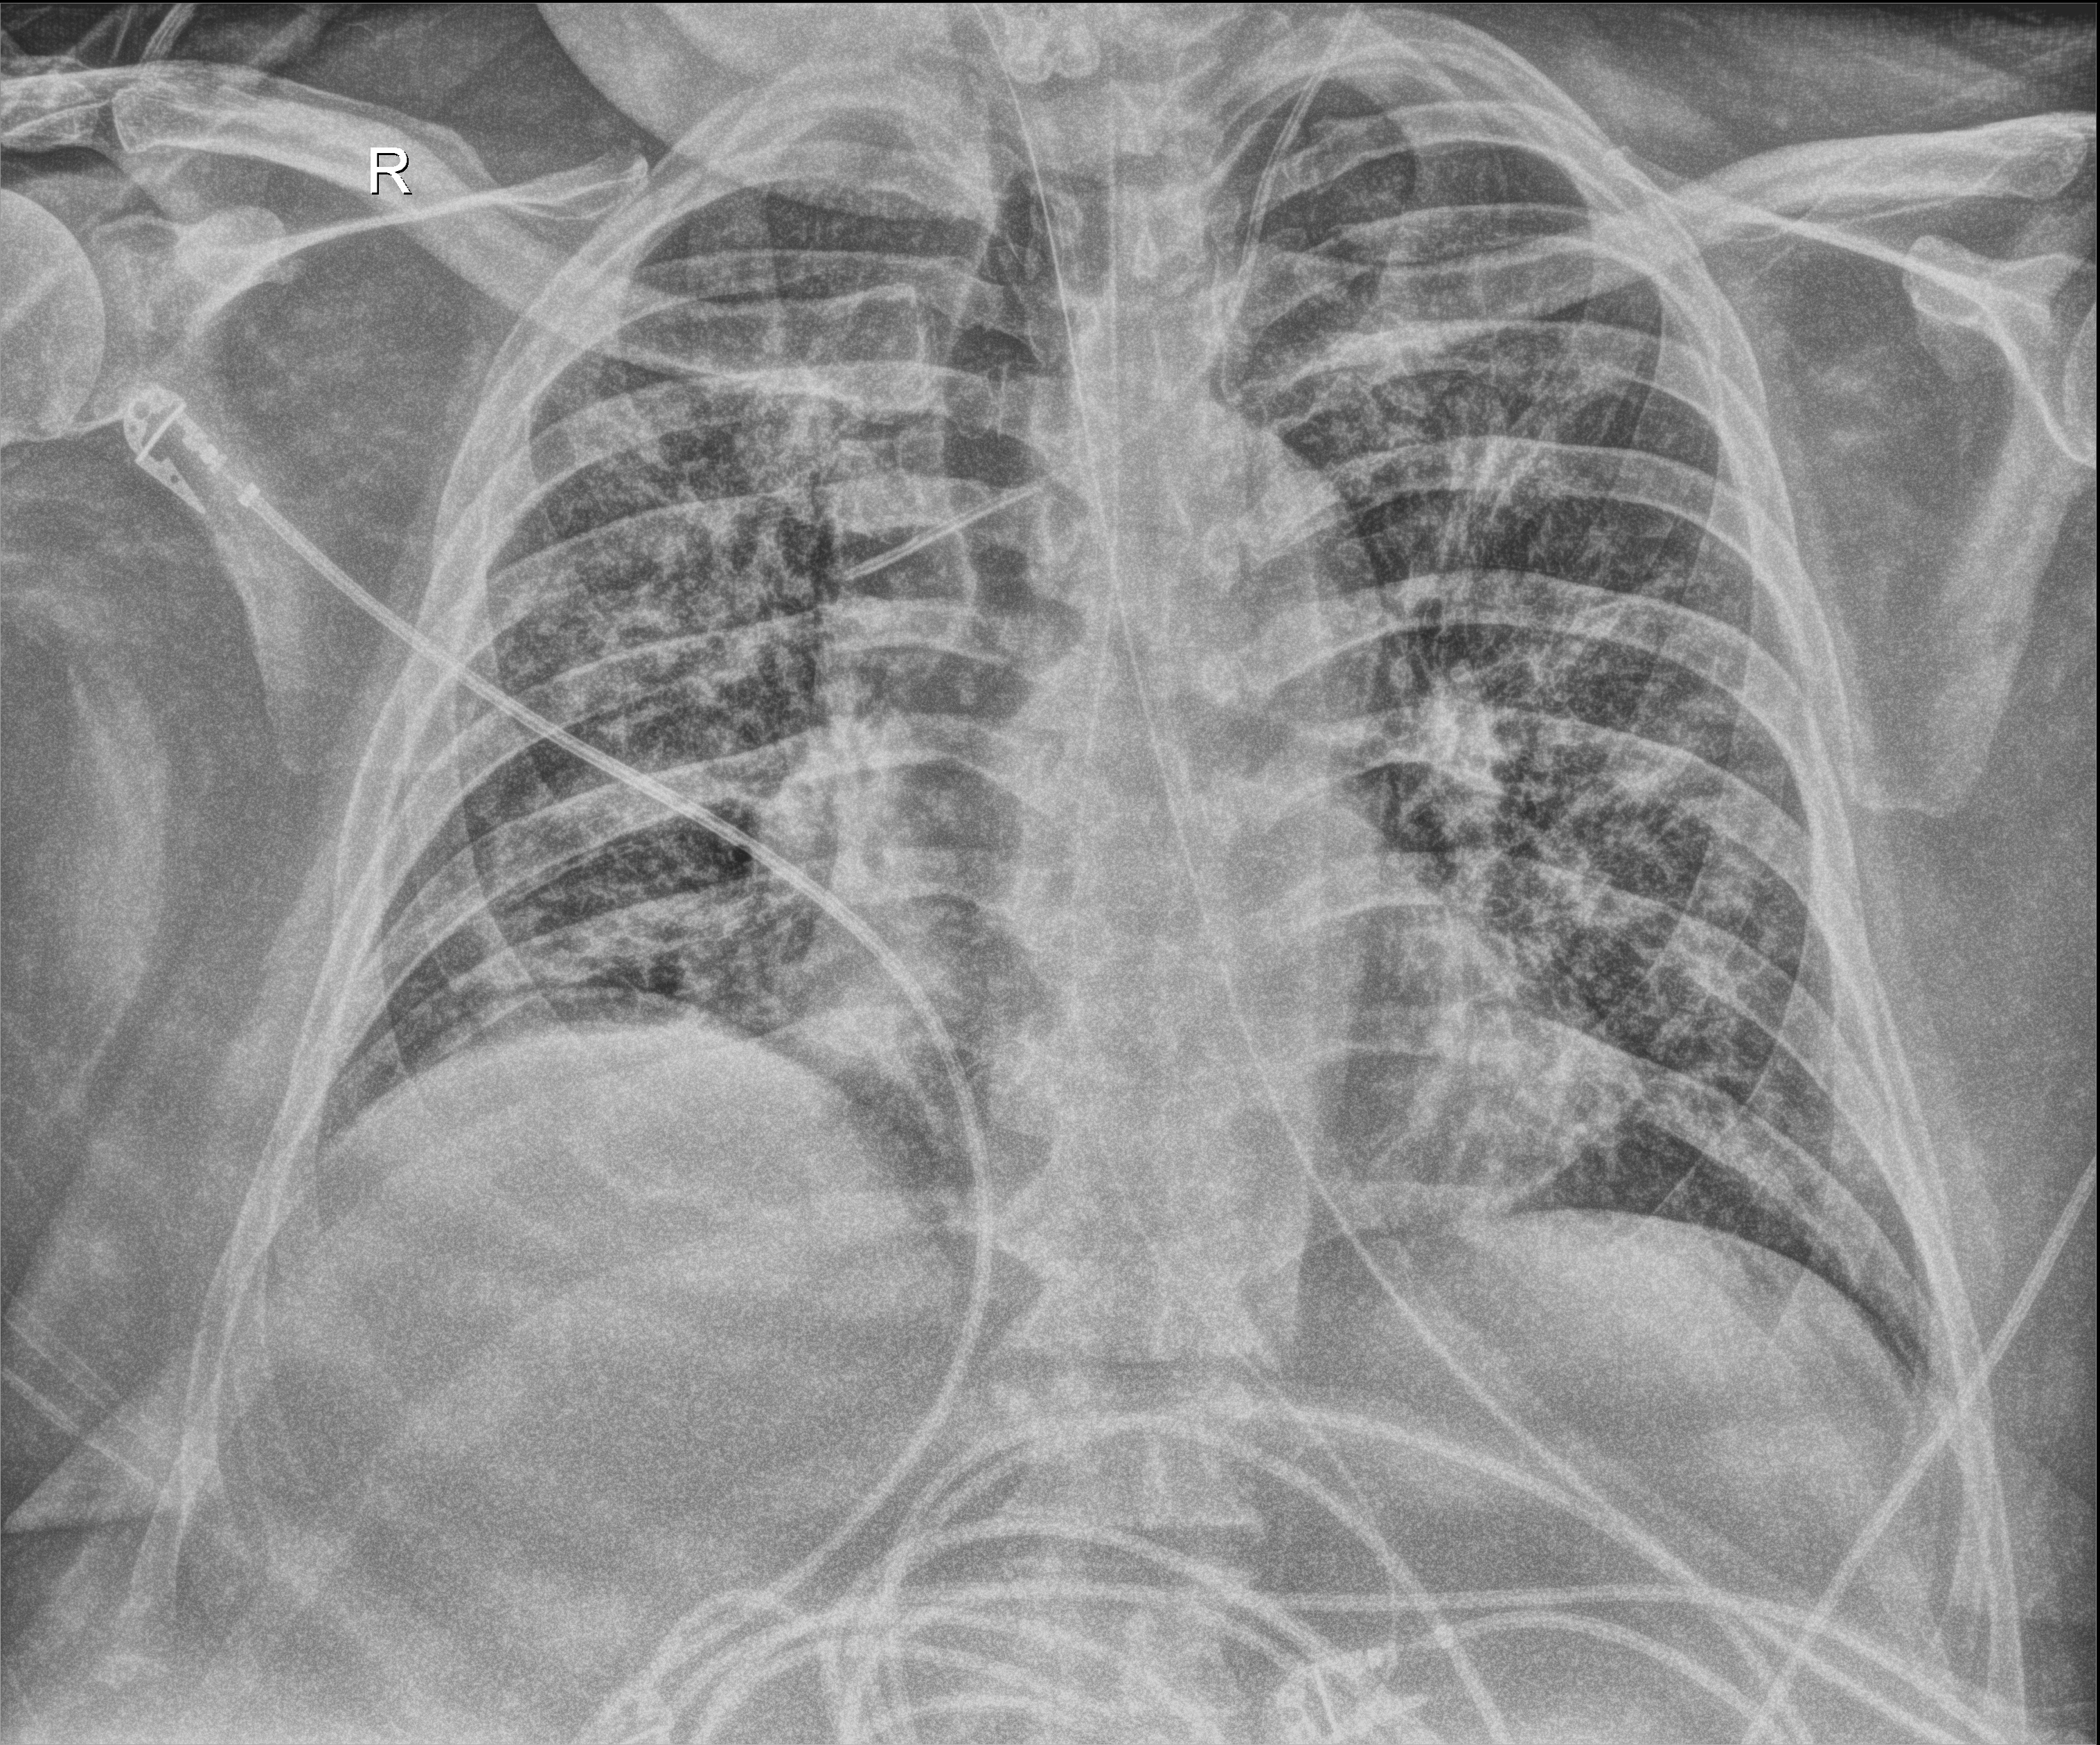
Bedside chest radiograph (digital radiography), anteroposterior (AP) projection. Male patient hospitalised with COVID-19, age 18–59 years.
From the hospital-stay record, not from the radiograph (when in the stay this image was taken is not recorded):
- length of hospital stay: 47 days